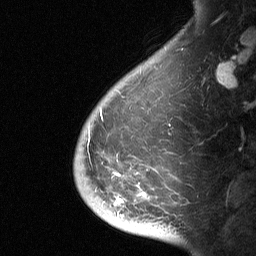
Breast MRI (dynamic contrast-enhanced), one sagittal slice. Slice 11 of 64 in the series (ordered by position). Dynamic contrast-enhanced study with each time point stored as its own series, time point 2 of 3 at this slice position (early post-contrast, ordered by acquisition time). 1.5 T. TE 4.8 ms, TR 27 ms. 256 × 256 image matrix, field of view 180 × 180 mm. Female patient, age 56 years. From the clinical record (not read from this slice): setting: breast cancer imaged before/during neoadjuvant chemotherapy; receptor status: HER2-positive.
Structures marked on this image (semi-automatically segmented with operator editing):
- analysis volume of interest (the breast-tissue region the enhancement analysis was run in; not a lesion): box from (x=73, y=144) to (x=182, y=229) px
- tumour enhancement mask (voxels above the 90 % enhancement threshold inside the analysis volume of interest): (x=107, y=159)–(x=143, y=204)